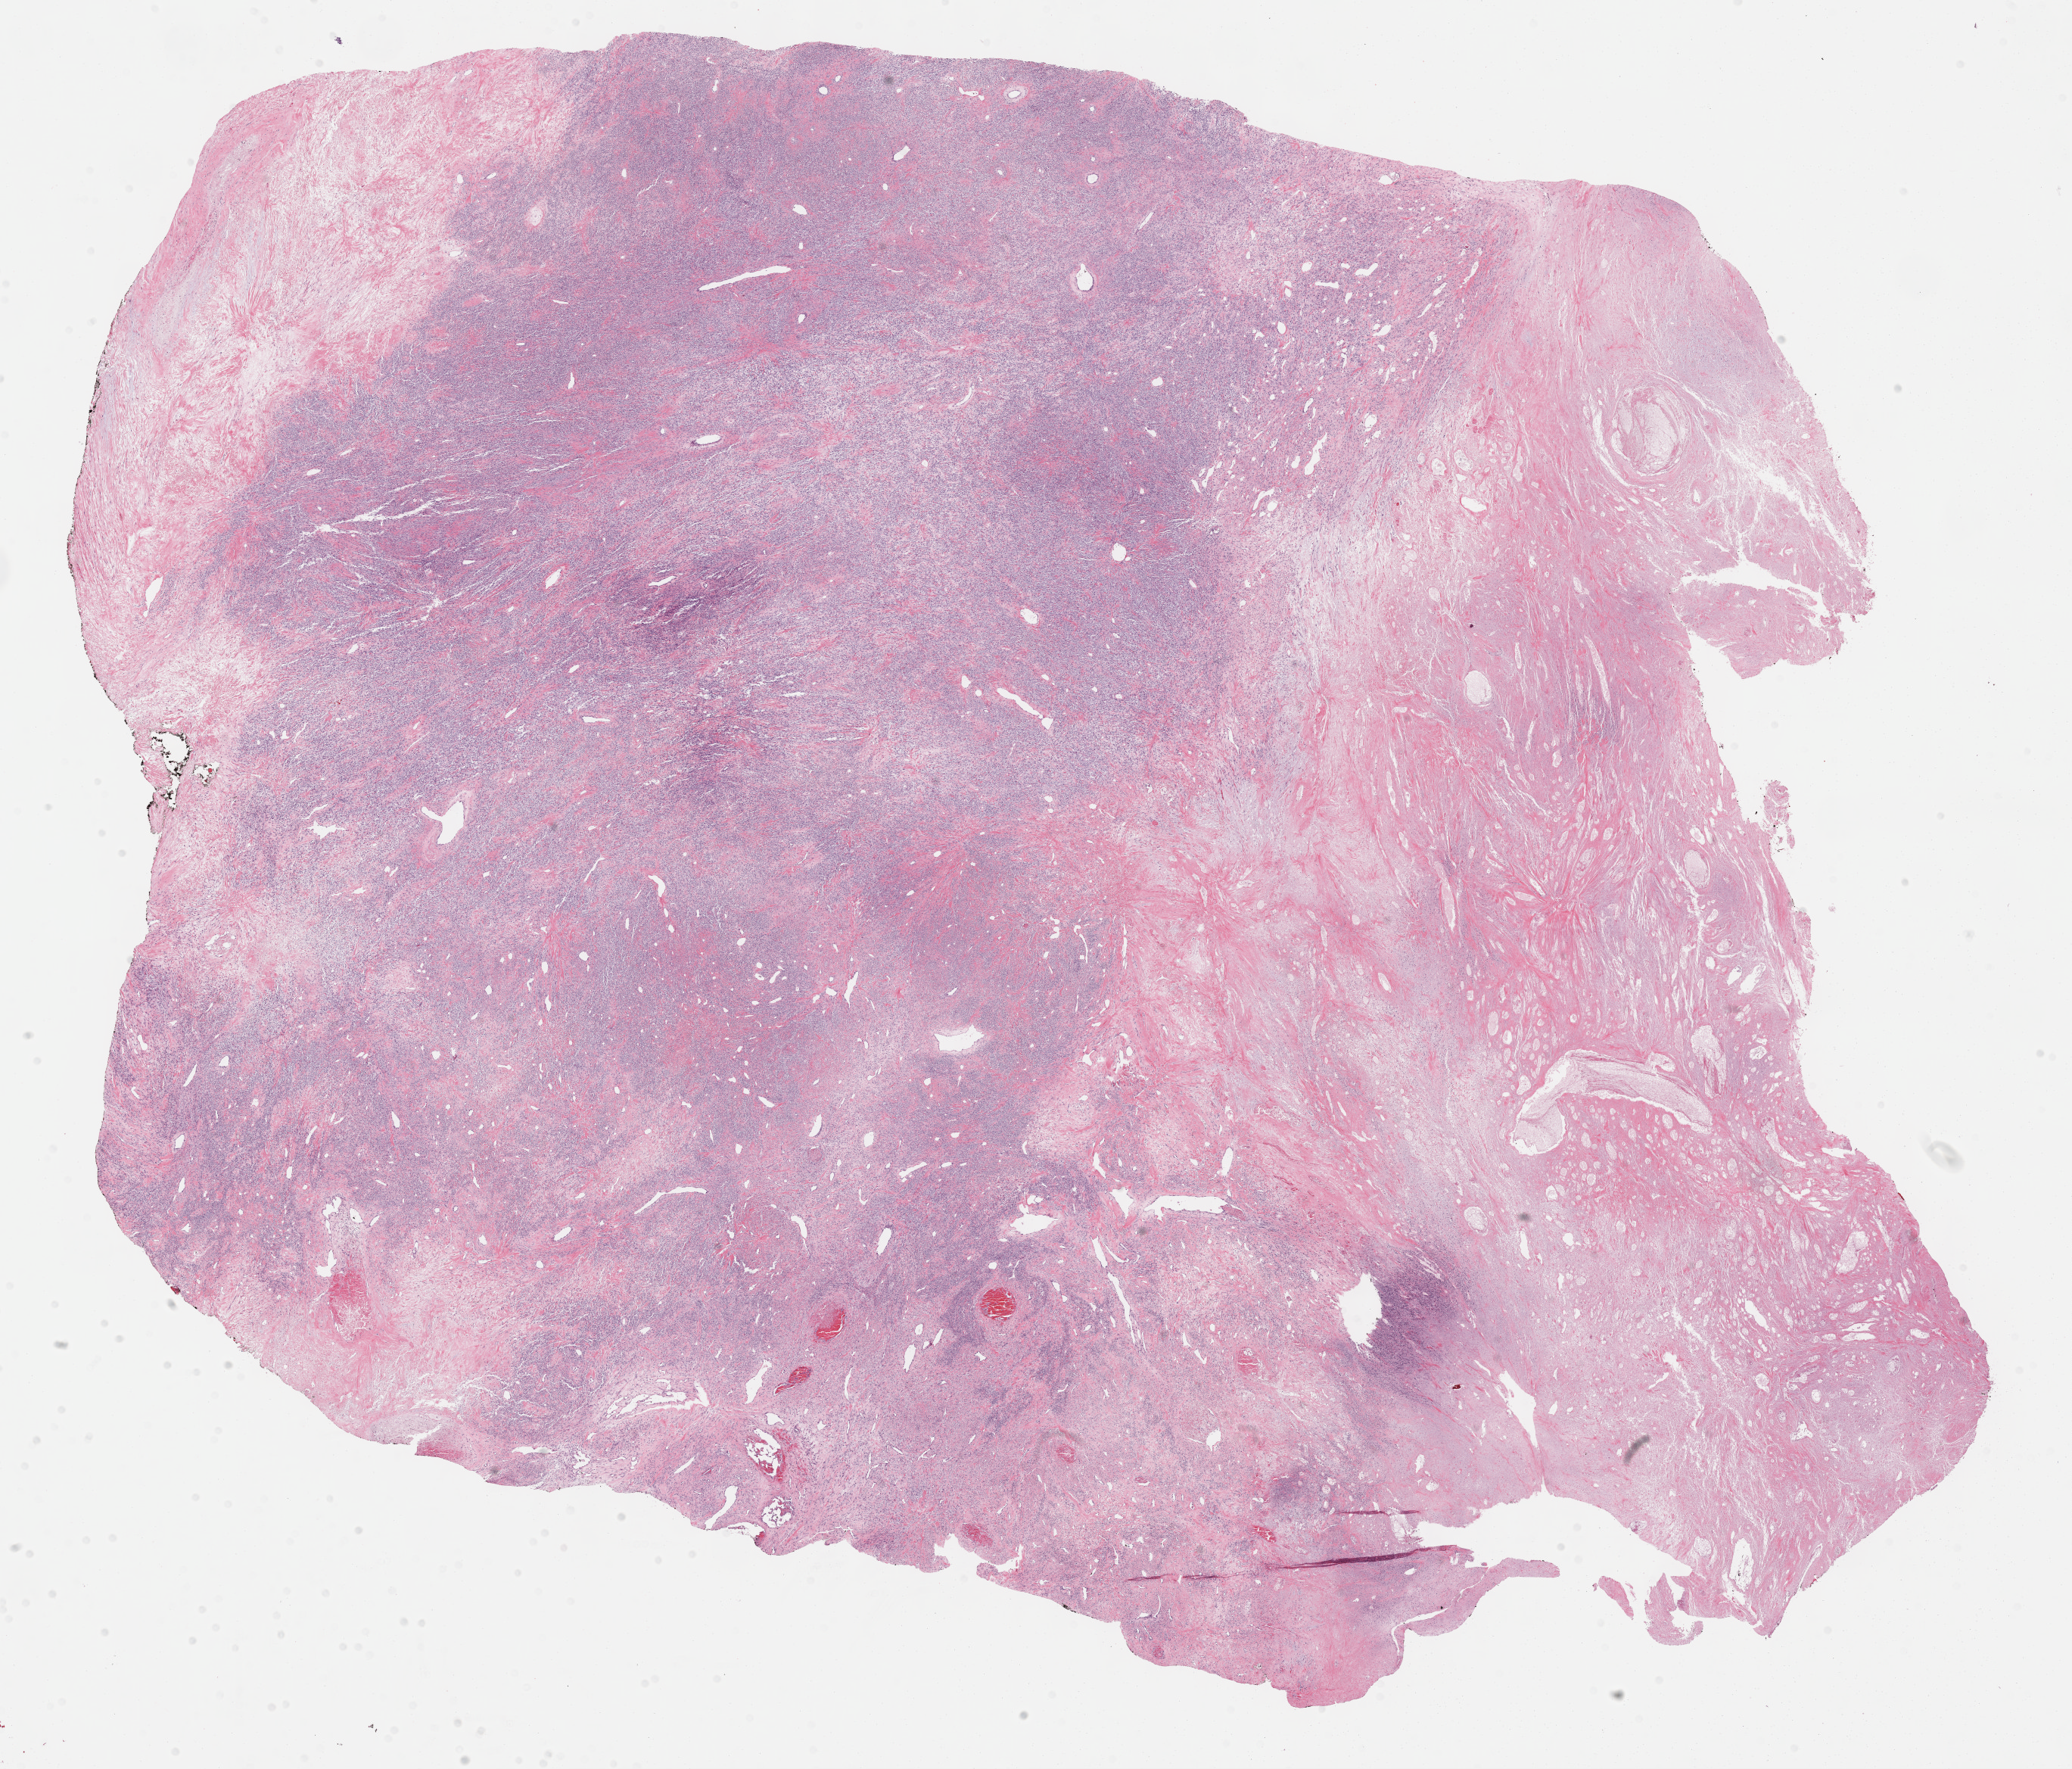
Whole-slide histology image, H&E-stained — low-resolution overview of the scanned area, about 22.1 x 18.9 mm. FFPE section. Retroperitoneum and peritoneum, primary tumour sample. Female patient; age at initial diagnosis 71 years.
Histologic diagnosis: Undifferentiated sarcoma (retroperitoneum).